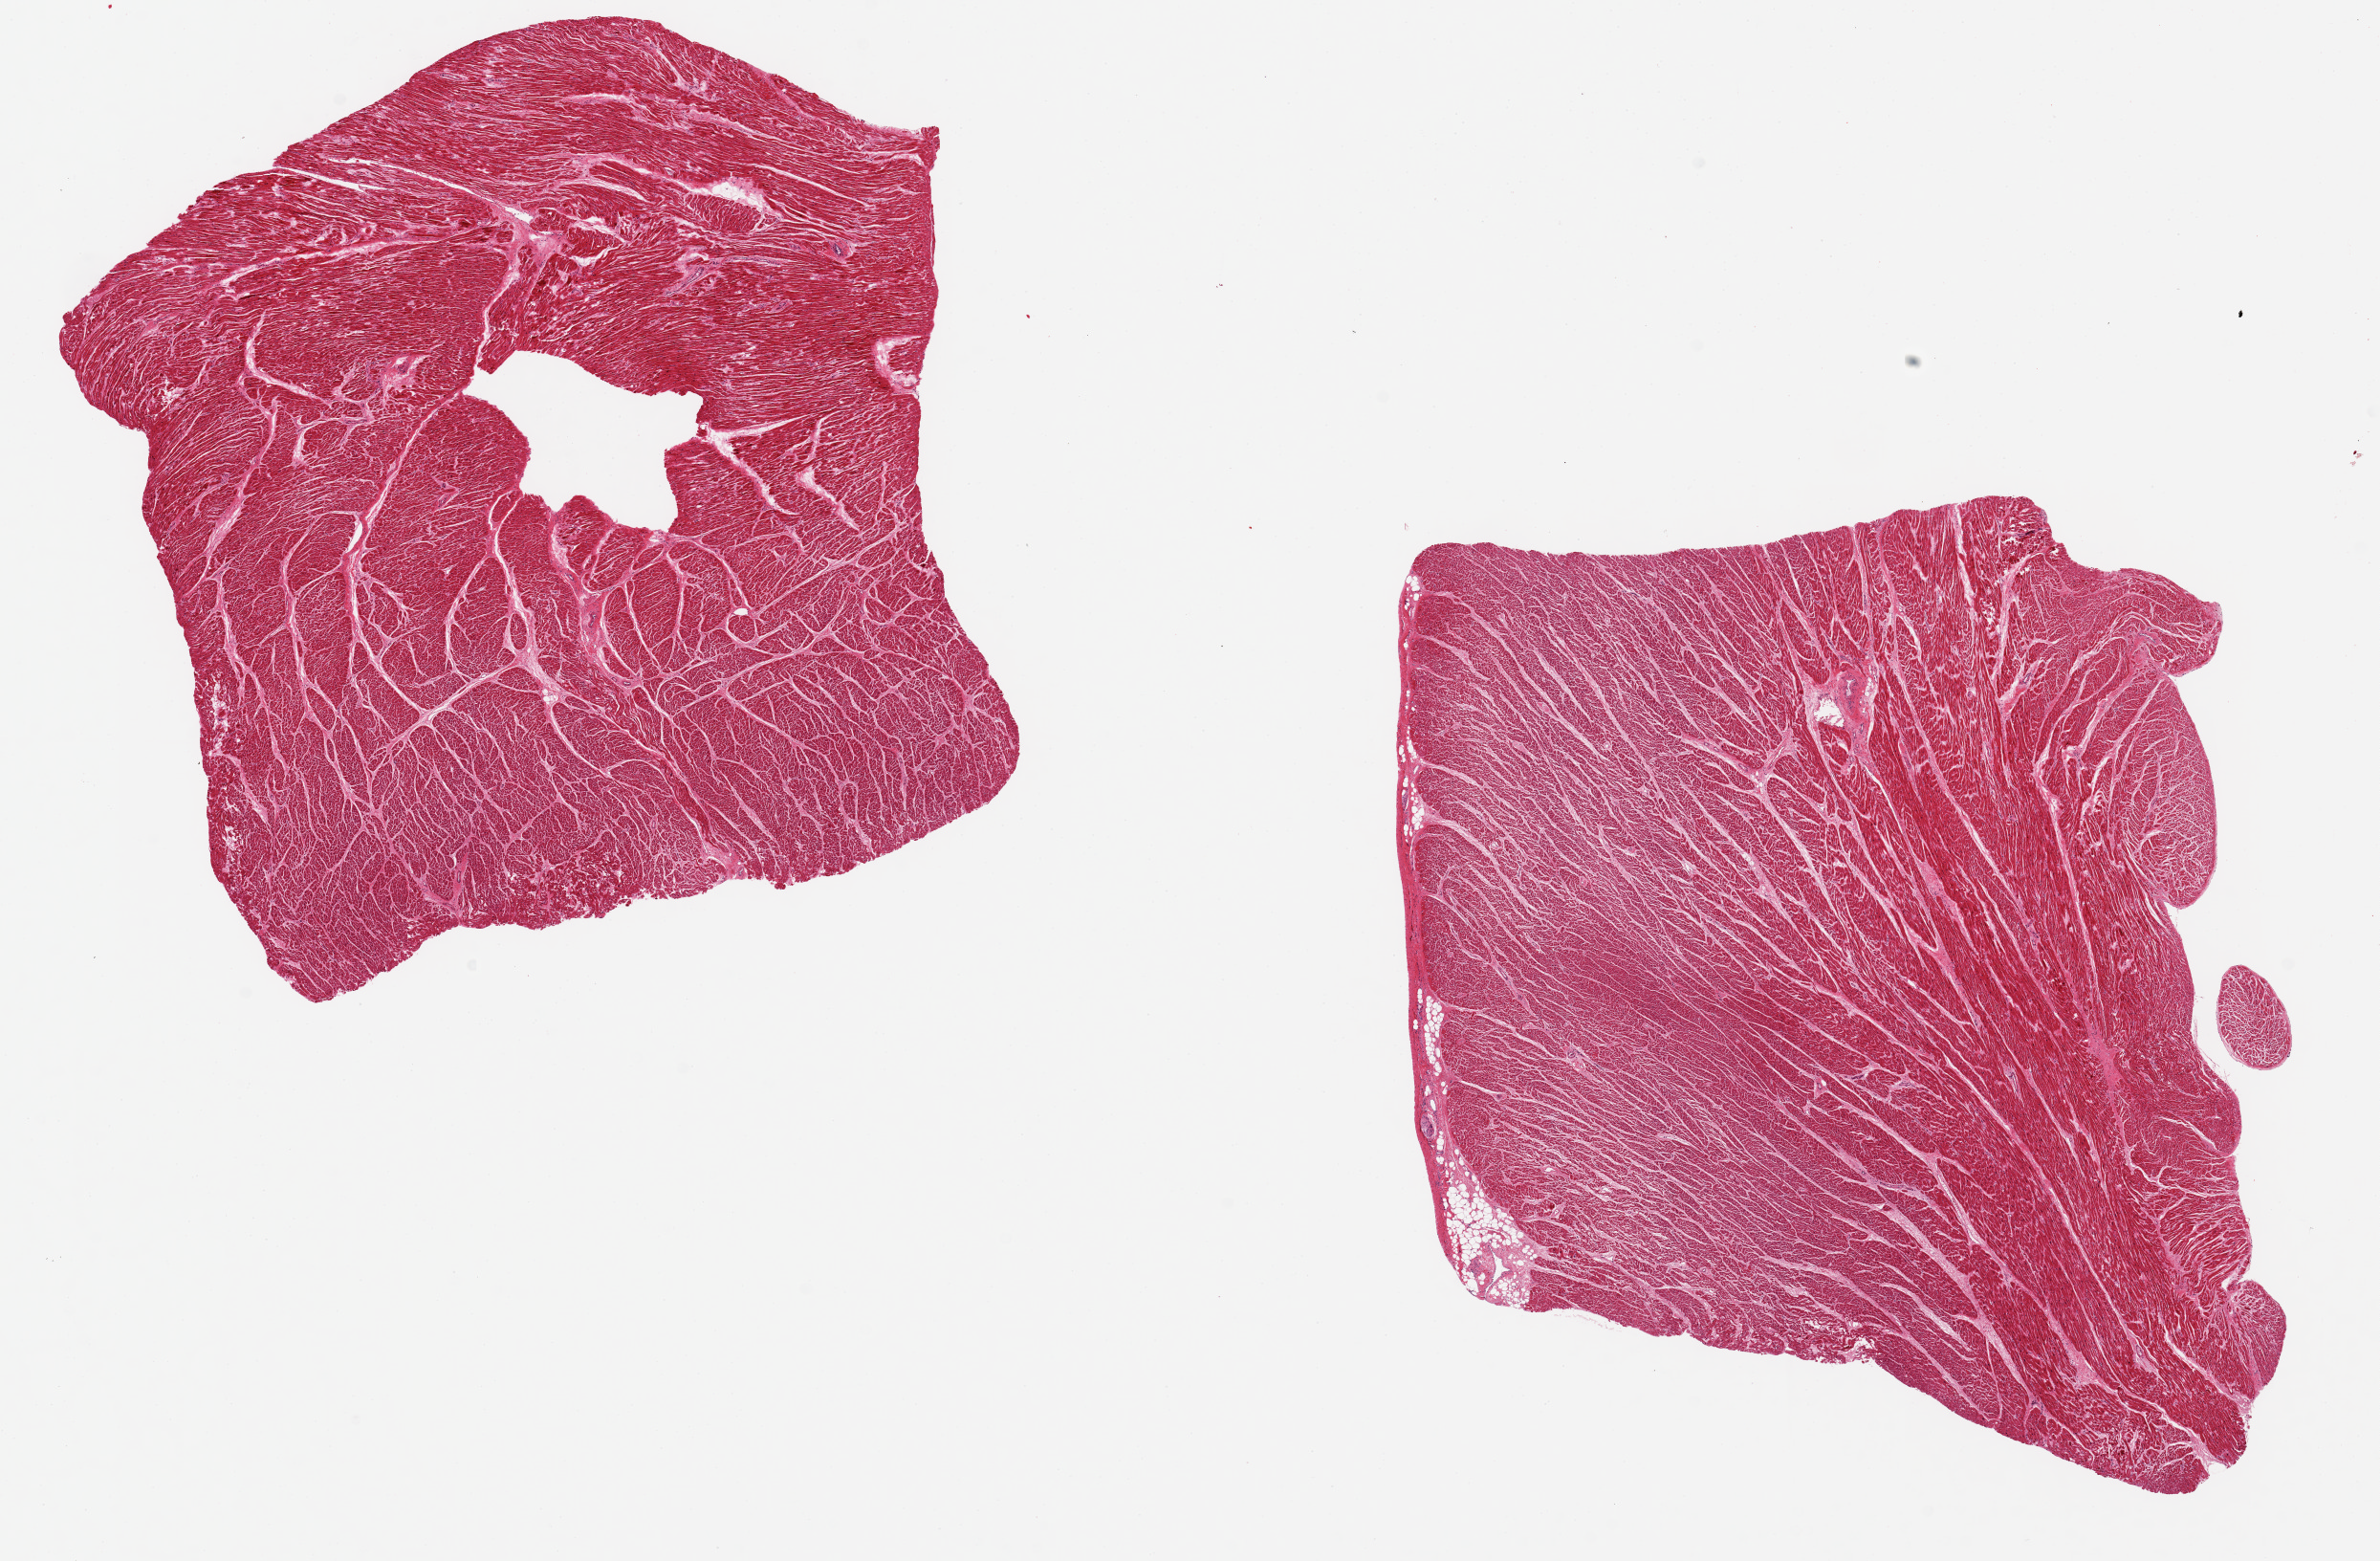
Whole-slide image, haematoxylin and eosin stain — whole scanned area (about 19.7 x 12.9 mm, slide scanned at 20x) shown as a low-resolution overview; PAXgene-fixed, paraffin-embedded tissue; sampled site (target tissue): heart; tissue donor sample. Male donor.
Pathologist's review note for this sample: 2 pieces ~7x6mm. No ischemic chenages noted.